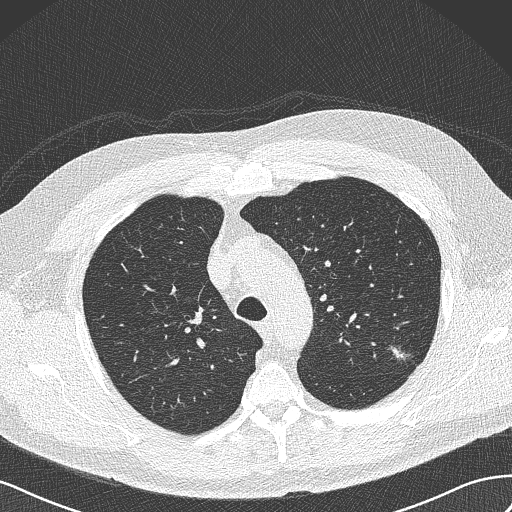
Low-dose screening chest CT, axial slice. Baseline annual screen. Lung window (W 1500 / L -600 HU). Lung (sharp) reconstruction kernel (B50f). Slice 110 of 462 in the series. Male, age 65 years at enrolment. Former smoker at enrolment.
- Lesion marked by an expert reader, box from (x=383, y=341) to (x=418, y=372) px.
- The screening reader recorded 3 non-calcified nodules or masses ≥4 mm on this exam; which of them this box marks is not recorded.
- Lung cancer was diagnosed 541 days after this screen: adenocarcinoma, NOS, left upper lobe, poorly differentiated (G3), stage IA (AJCC 6th edition), 13 mm at pathology.